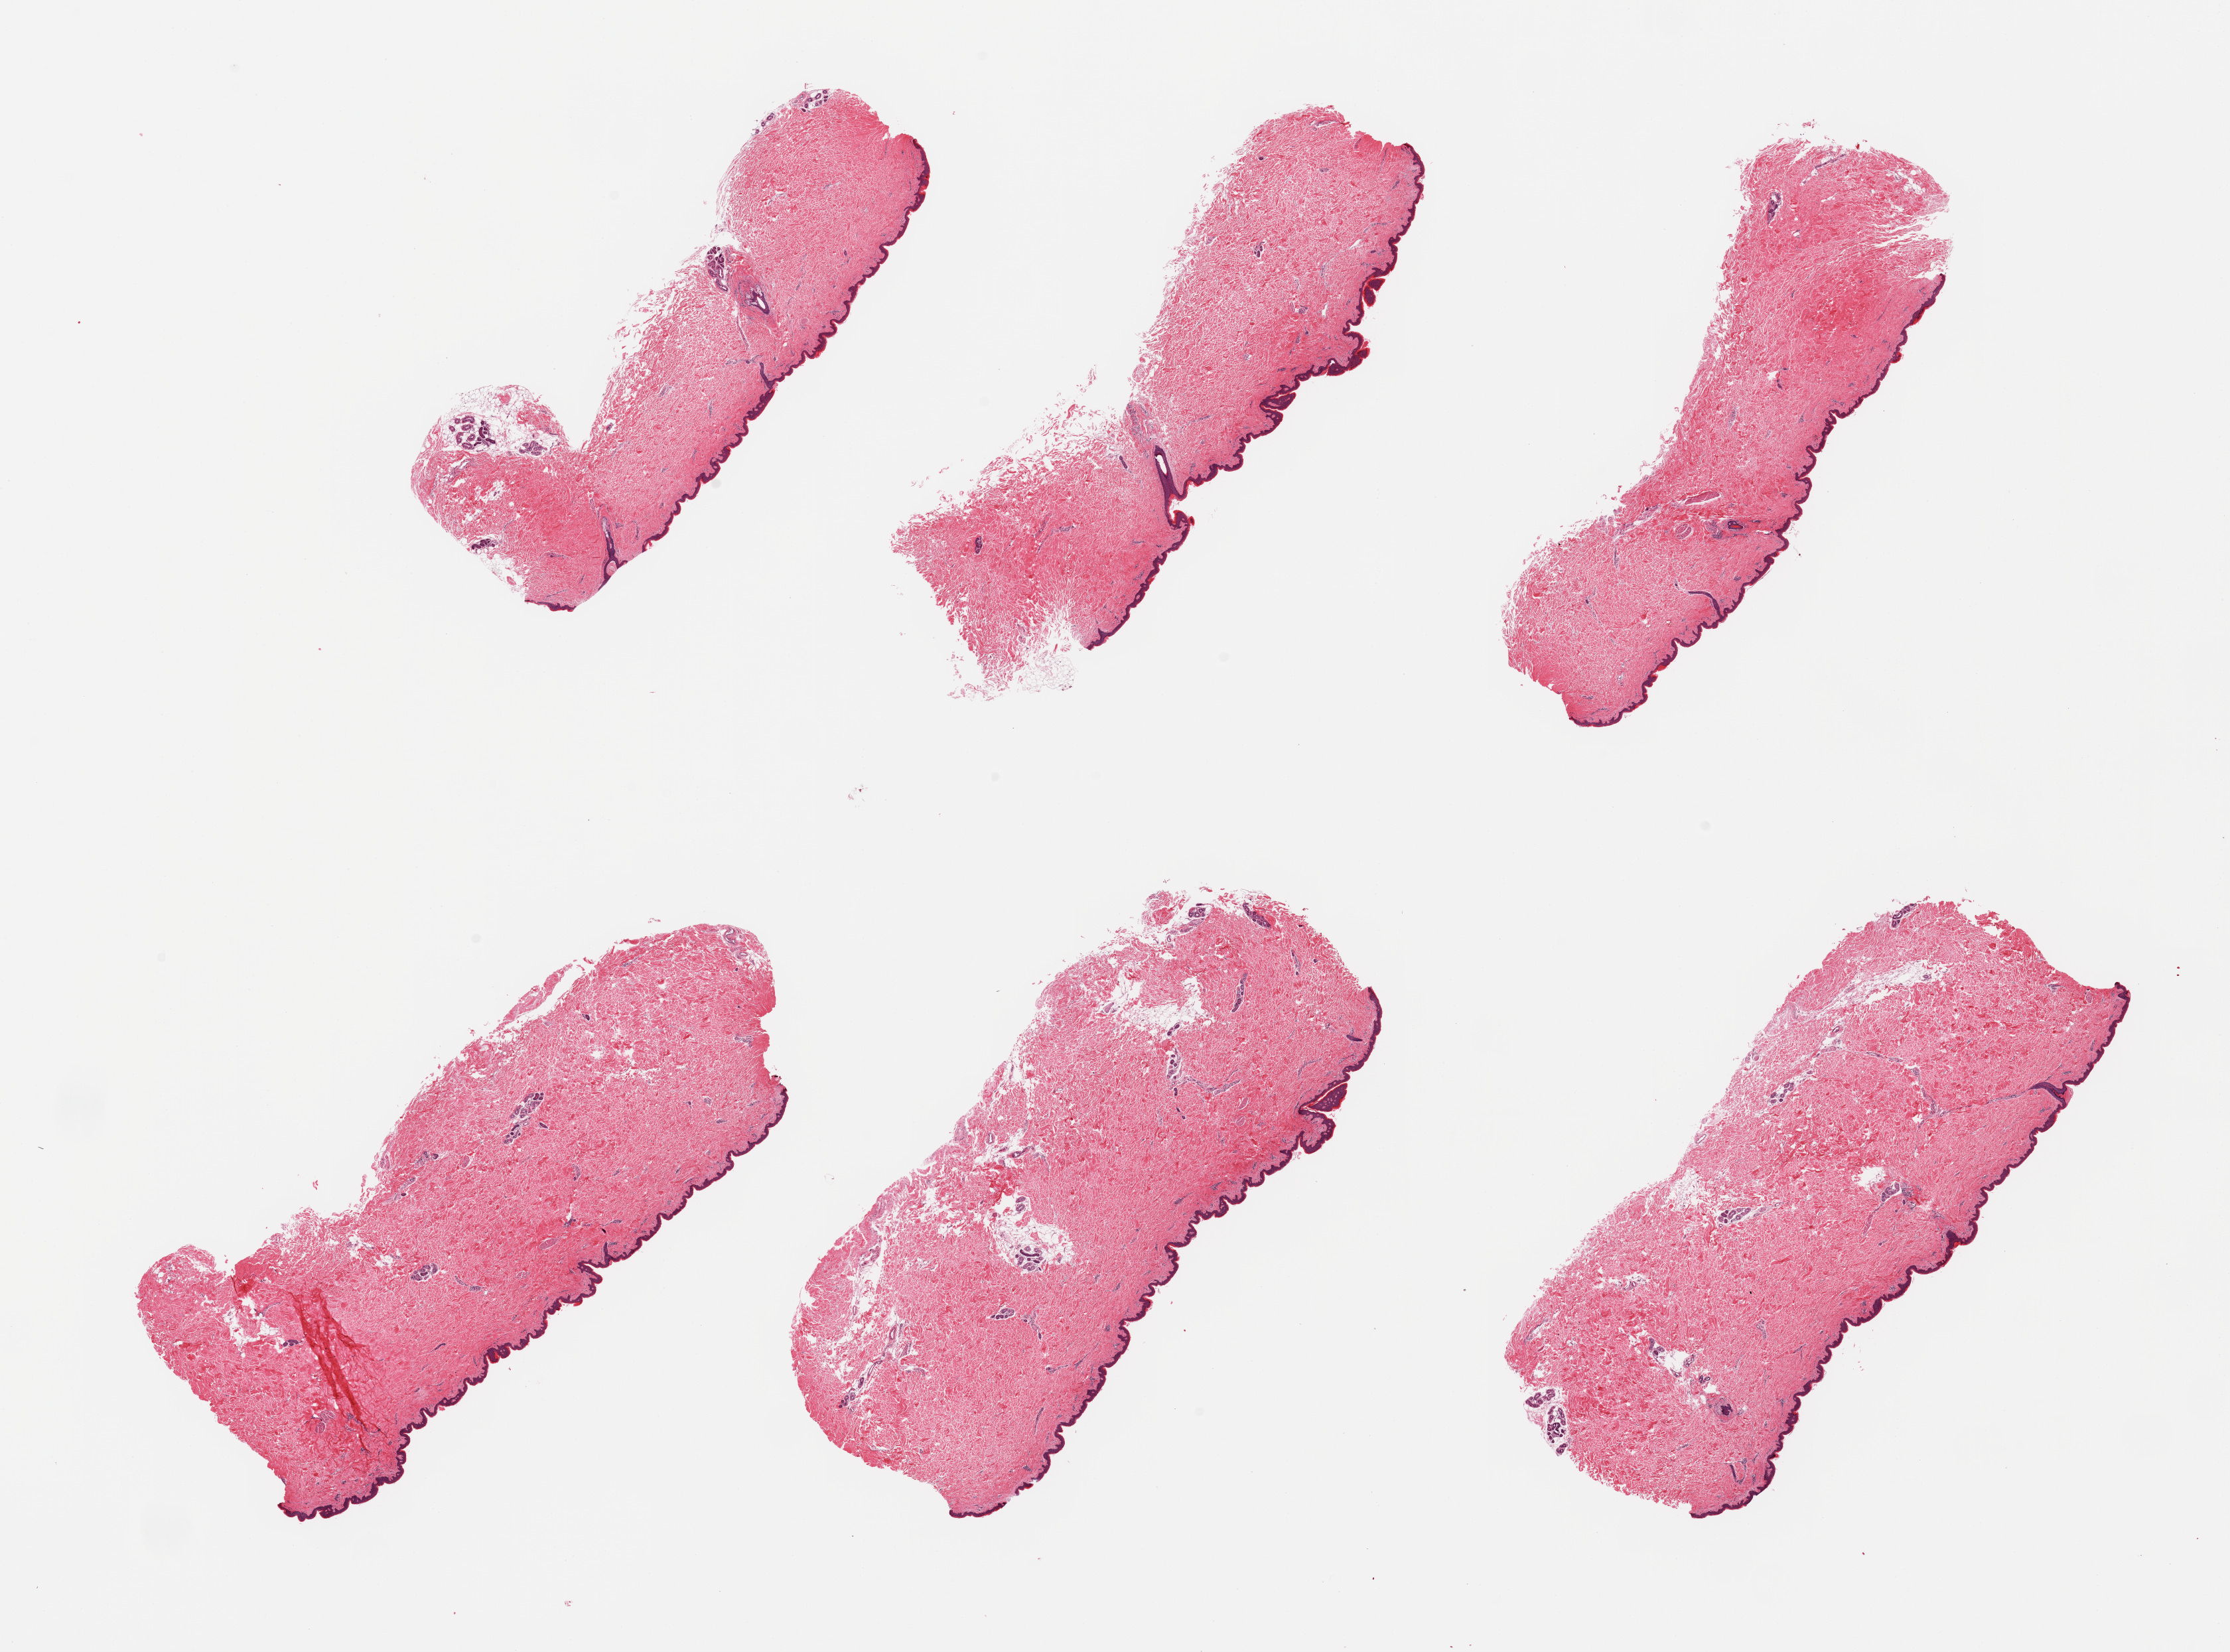
Hematoxylin and eosin (H&E) whole-slide image — low-resolution overview of the scanned area, about 26.6 x 19.7 mm; PAXgene-fixed, paraffin-embedded tissue; target tissue: skin of suprapubic region; tissue donor sample.
* pathologist's review note for this sample: 6 pieces, minimal dermal fat; squamous epithelium is ~60 microns